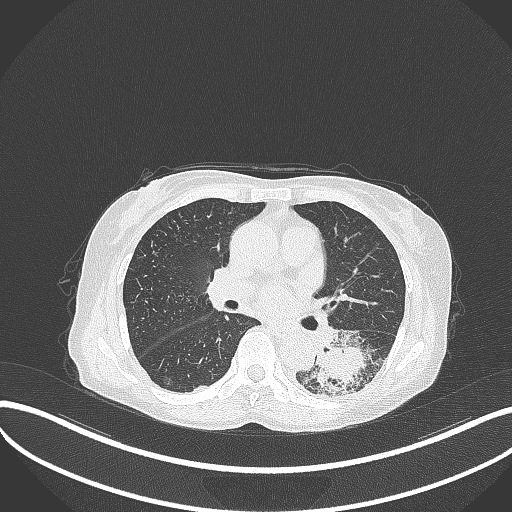
Chest CT, one axial slice. Position 170 of 370 along the scan axis. 120 kVp. Lung window (W 1500 / L -600 HU). 512 × 512 image matrix, field of view 400 × 400 mm. Female patient, age 78 years. From the clinical record (not read from this slice): clinical TNM (as recorded): T3 N0 M1.
Structures marked on this image (rectangle marked by the reading radiologist):
- lung tumour (recorded histology: squamous cell carcinoma): bounding box [x1, y1, x2, y2] px = [308, 331, 387, 393]